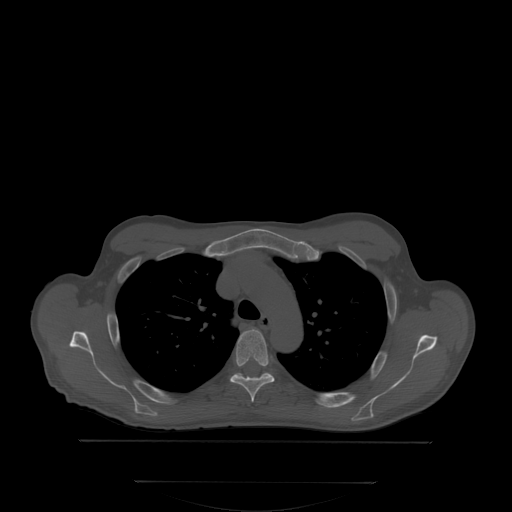
CT including the spine, one axial slice; slice 257 of 350 in the series (ordered by position); bone window (W 1800 / L 400 HU); 512 × 512 image matrix, field of view 500 × 500 mm. Patient: male, 58 years. Case-level facts recorded for this patient, not image findings: primary cancer: prostate; vertebrae with lytic lesions (as recorded): L1.
Structures marked on this image (semi-automatic segmentation, software-assisted and operator-edited):
- T4 vertebra: bounding box [x1, y1, x2, y2] px = [231, 329, 275, 402]
- T5 vertebra: [238, 373, 268, 376]